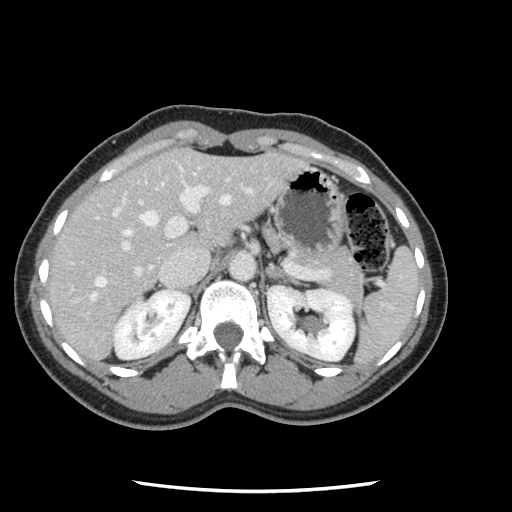
Contrast-enhanced abdominal CT, one axial slice. Slice 78 of 134 in the series (ordered by position). 120 kVp. Intravenous contrast given. Soft-tissue window (W 400 / L 40 HU). 2.5 mm slice thickness. 512 × 512 image matrix, field of view 330 × 330 mm. Female patient, age 43 years. From the clinical record (not read from this slice): diagnosis: colorectal cancer liver metastases, imaged before liver resection; multiple liver metastases: yes; largest metastasis: 3.4 cm; disease in both lobes: yes.
Annotated regions visible in this slice (expert manual segmentation):
- hepatic veins: box from (x=90, y=174) to (x=231, y=301) px
- liver: (x=48, y=150)–(x=300, y=361)
- planned liver remnant (the part of the liver to remain after resection): (x=48, y=153)–(x=189, y=305)
- portal vein (with intrahepatic branches): (x=71, y=166)–(x=253, y=291)